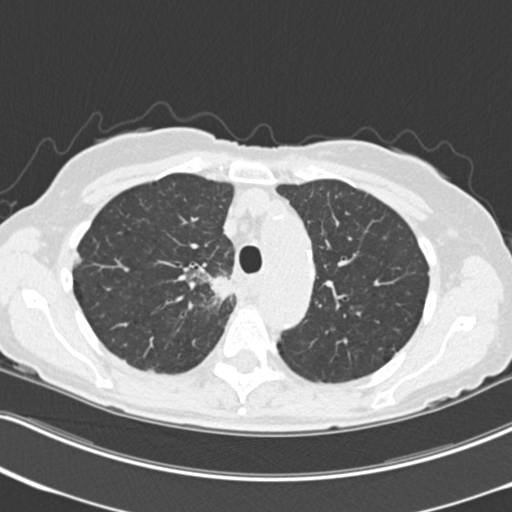
Low-dose screening chest CT, one axial slice. Position 167 of 226 along the scan axis. 120 kVp. Lung window (W 1500 / L -600 HU). 2 mm slice thickness. 512 × 512 image matrix, field of view 322 × 322 mm.
Annotated regions visible in this slice (outlined manually by an expert reader):
- lesion 1 (tumor, mediastinum): bounding box (x1, y1, x2, y2) in pixels: (211, 276, 231, 301)